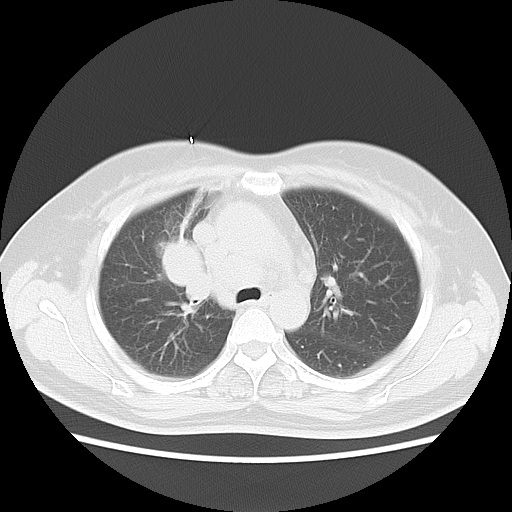
Chest CT, one axial slice; slice 9 of 18 in the series (ordered by position); reconstruction kernel LUNG; 120 kVp; lung window (W 1500 / L -600 HU); 512 × 512 image matrix. Female patient, age 54 years. Case-level facts recorded for this patient, not image findings: clinical TNM (as recorded): T2 N3 M0; histopathological grade: G3.
Outlined on this slice (bounding box drawn by a radiologist):
- lung tumour (recorded histology: small cell carcinoma): bounding box <154,236,210,303> (left, top, right, bottom; pixels)